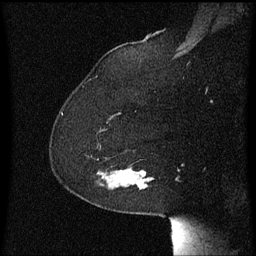
Breast MRI (dynamic contrast-enhanced), one sagittal slice; slice 45 of 60 in the series (ordered by position); dynamic contrast-enhanced series, image 2 of 3 at this slice position (ordered by acquisition); 1.5 T; TE 4.2 ms, TR 8.4 ms; 2 mm slice thickness; 256 × 256 image matrix. Patient: female, 59 years.
Structures marked on this image (semi-automatic segmentation, software-assisted and operator-edited):
- analysis volume of interest (the breast-tissue region the enhancement analysis was run in; not a lesion): bounding box (x1, y1, x2, y2) in pixels: (98, 168, 153, 191)
- tumour enhancement mask (voxels above the 70 % enhancement threshold inside the analysis volume of interest): (140, 172, 153, 183)